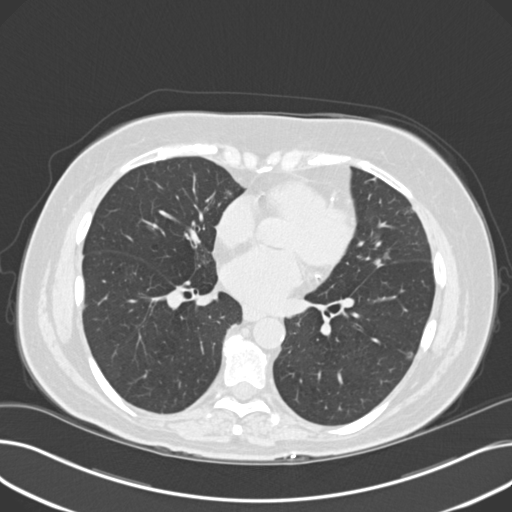
Axial slice from a low-dose chest CT screening exam, third screening round (two years after baseline), lung window (W 1500 / L -600 HU), 2 mm slice thickness, standard (soft-tissue) reconstruction kernel (B30f), 512 × 512 image matrix, field of view 372 × 372 mm. Female, age 60 years at enrolment.
Expert reader's lesion annotation, bounding box <359,247,405,283> (left, top, right, bottom; pixels). The screening reader recorded 8 non-calcified nodules or masses ≥4 mm on this exam (right upper lobe, lingula, lingula, right middle lobe, right lower lobe, left lower lobe, left lower lobe, left lower lobe); which of them this box marks is not recorded. Later outcome: lung cancer diagnosed 176 days after this screen — non-small cell carcinoma, left upper lobe, poorly differentiated (G3), stage IB (AJCC 6th edition), 7 mm at pathology.